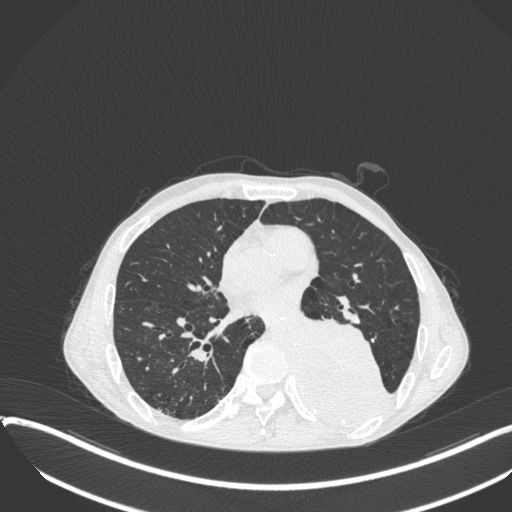
Chest CT, one axial slice. Position 169 of 400 along the scan axis. 120 kVp. Lung window (W 1500 / L -600 HU). 1 mm slice thickness. 512 × 512 image matrix, field of view 400 × 400 mm. Patient: male, 57 years. From the clinical record (not read from this slice): clinical TNM (as recorded): T4 N0 M0.
Outlined on this slice (rectangle marked by the reading radiologist):
- lung tumour (recorded histology: squamous cell carcinoma): bounding box <296,304,395,429> (left, top, right, bottom; pixels)